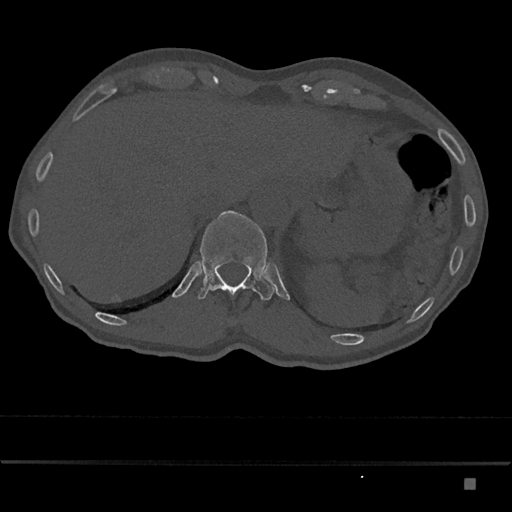
CT including the spine, one axial slice; position 619 of 797 along the scan axis; bone window (W 1800 / L 400 HU); 512 × 512 image matrix, field of view 390 × 390 mm. Male patient, age 72 years. Case-level facts recorded for this patient, not image findings: primary cancer: prostate.
Annotated regions visible in this slice (semi-automatically segmented with operator editing):
- T12 vertebra: bounding box [x1, y1, x2, y2] px = [198, 210, 275, 301]